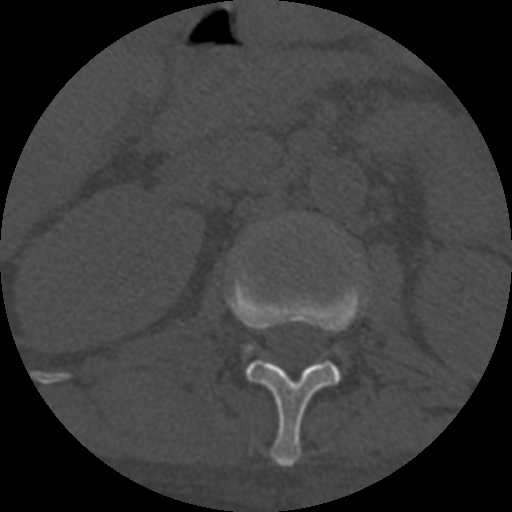
CT including the spine, one axial slice. One of 3 acquisitions stored at this slice position. Bone window (W 1800 / L 400 HU). 1.25 mm slice thickness. 512 × 512 image matrix, field of view 160 × 160 mm. Patient age 55 years. Case-level facts recorded for this patient, not image findings: primary cancer: colon; vertebrae with lytic lesions (as recorded): T12, L1, L5.
Outlined on this slice (semi-automatic segmentation, software-assisted and operator-edited):
- L1 vertebra: bounding box <228,266,367,467> (left, top, right, bottom; pixels)
- L2 vertebra: <248,349,250,351>